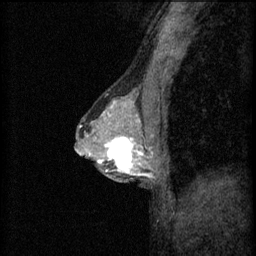
Breast MRI (dynamic contrast-enhanced), one sagittal slice; position 35 of 60 along the scan axis; 3 images stored at this slice position (order not interpretable as contrast timing); 1.5 T; TE 4.2 ms, TR 8.2 ms; 2 mm slice thickness; 256 × 256 image matrix, field of view 180 × 180 mm. Patient: female, 44 years.
Structures marked on this image (semi-automatically segmented with operator editing):
- analysis volume of interest (the breast-tissue region the enhancement analysis was run in; not a lesion): bounding box (x1, y1, x2, y2) in pixels: (102, 132, 151, 181)
- tumour enhancement mask (voxels above the 70 % enhancement threshold inside the analysis volume of interest): (102, 136, 149, 177)